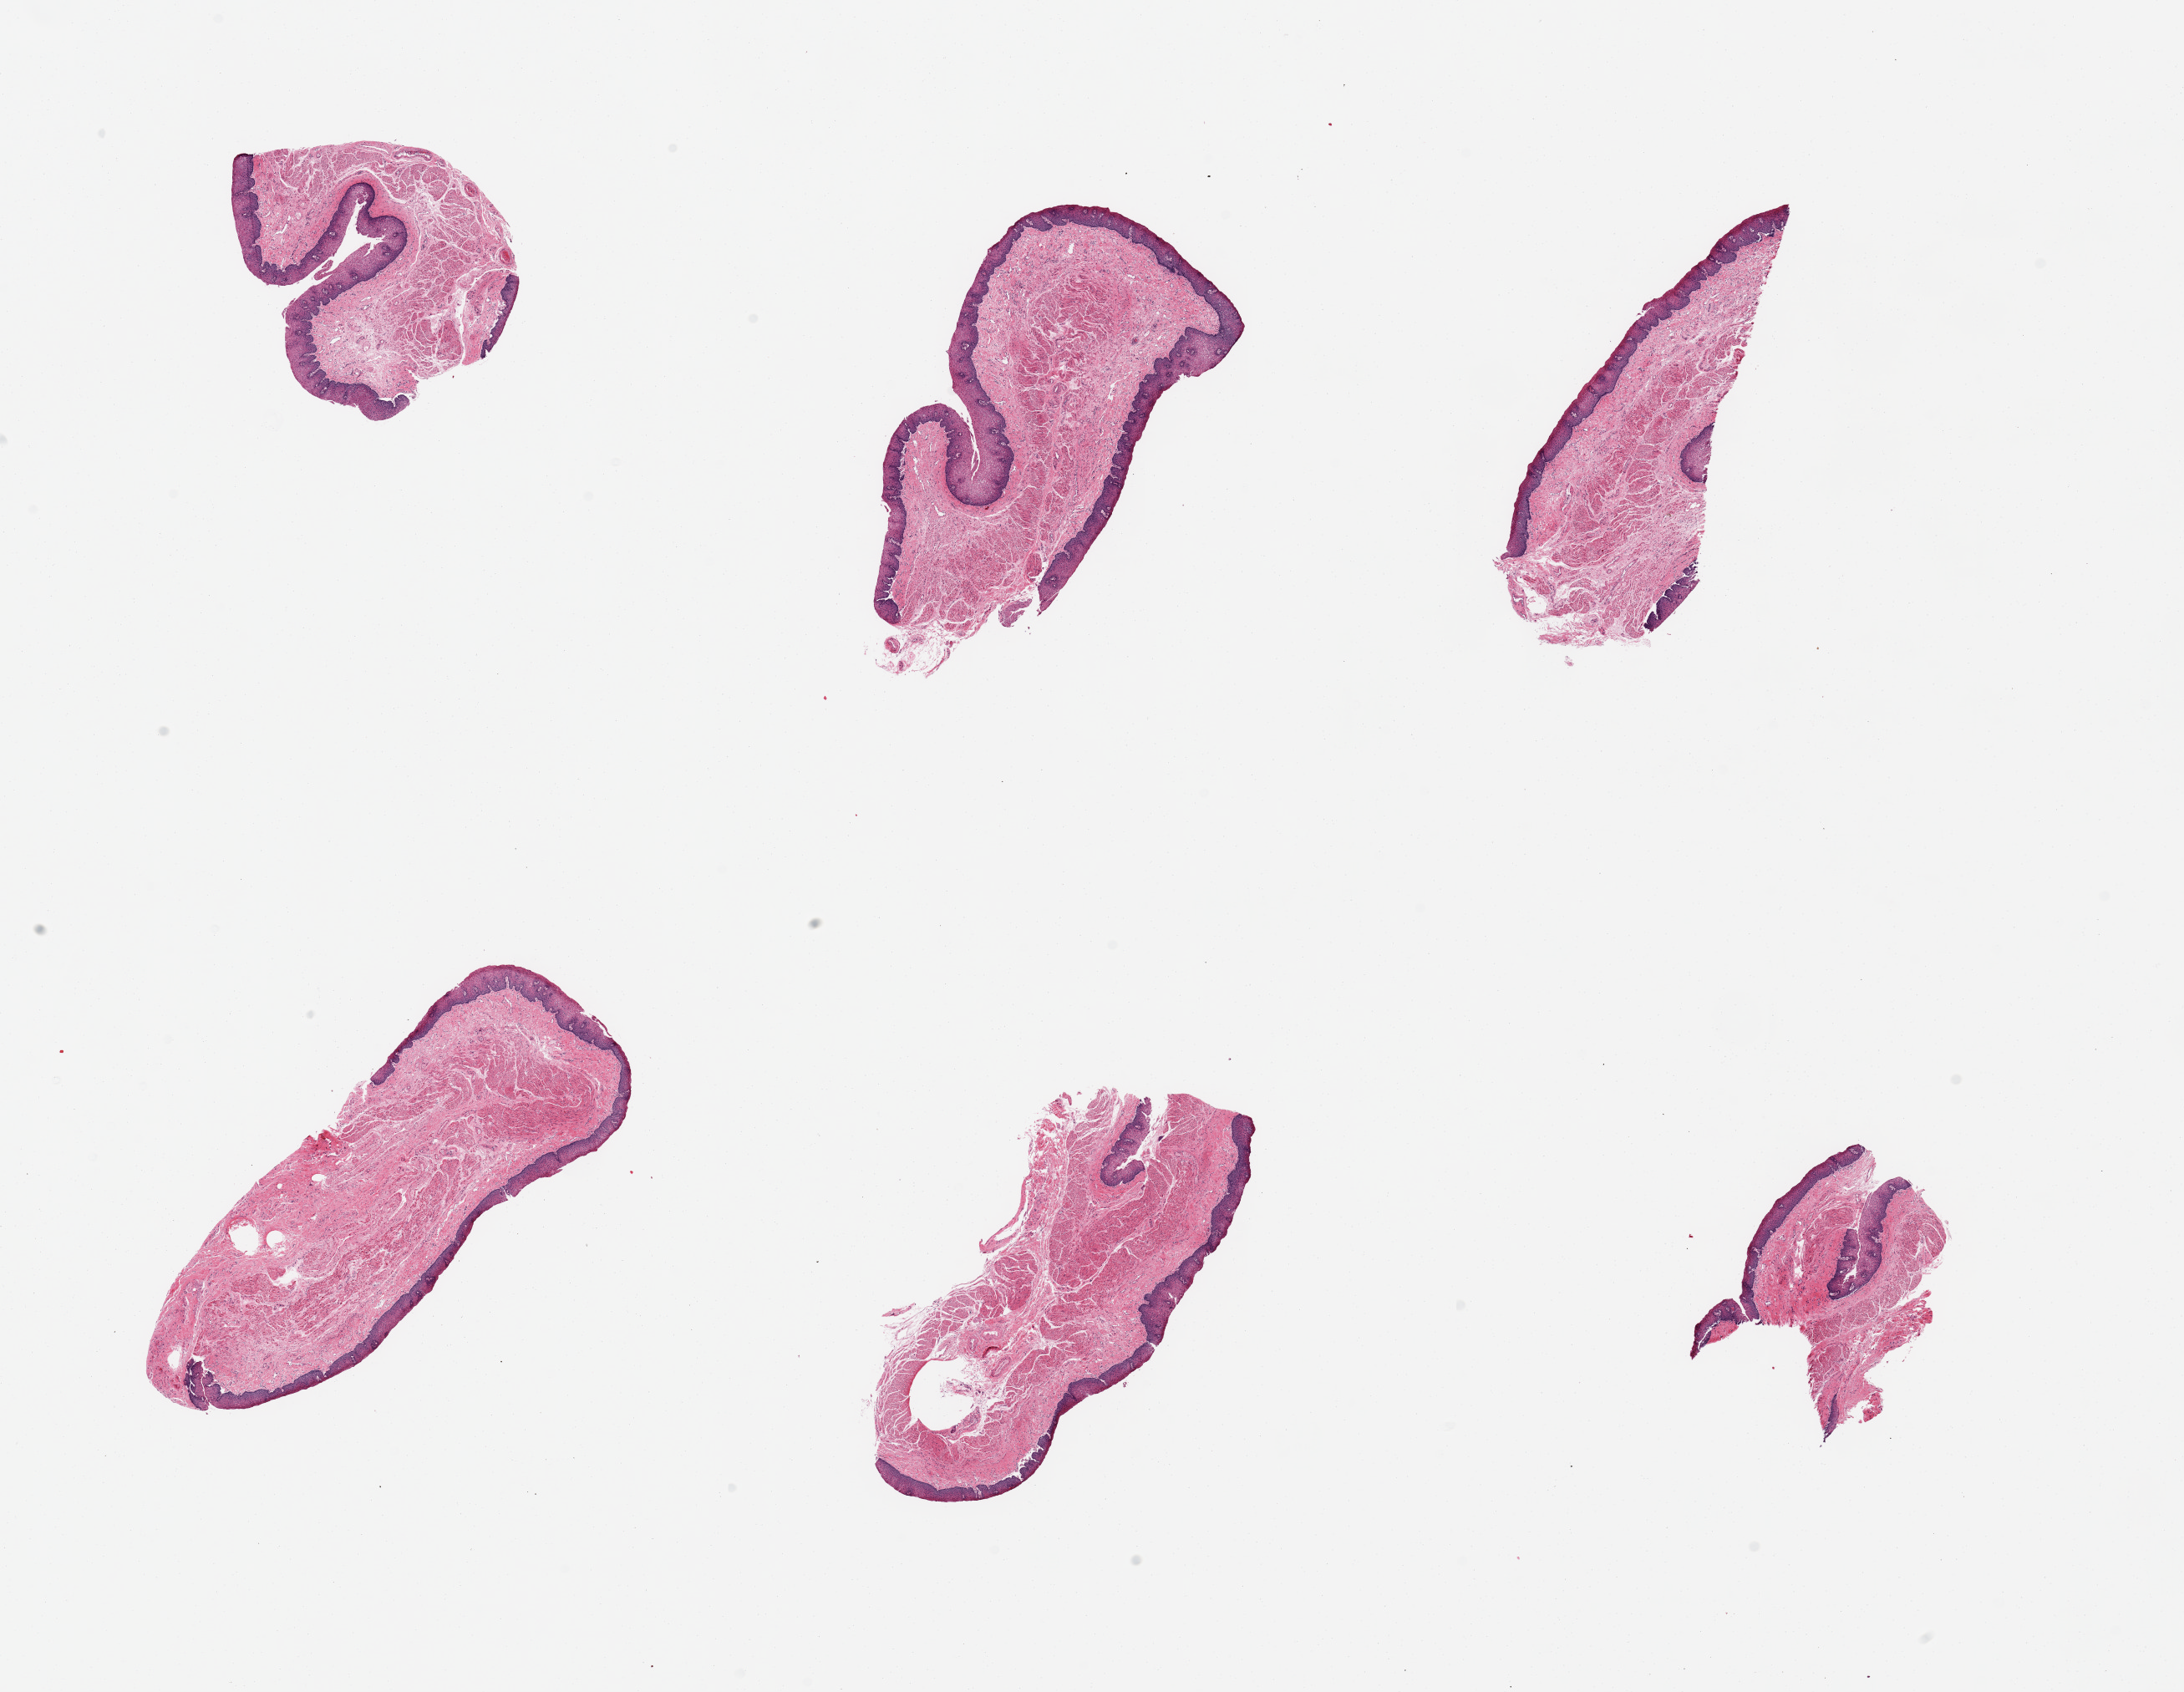
Digitized hematoxylin and eosin (H&E)-stained section, brightfield, whole scanned area (about 20.7 x 16.0 mm, from a 20x scan) shown as a low-resolution overview; PAXgene-fixed paraffin-embedded (PFPE) section; sampled site (target tissue): esophageal mucous membrane; donor tissue sample.
Review note (as recorded): 6 pieces.